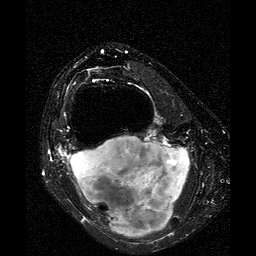
MRI of an extremity soft-tissue mass, one axial slice; slice 17 of 25 in the series (ordered by position); T2-weighted fat-saturated; 256 × 256 image matrix, field of view 160 × 160 mm. Female patient. From the clinical record (not read from this slice): histological type: liposarcoma; site of the primary tumour: right thigh.
Outlined on this slice (outlined manually by an expert reader):
- gross tumour volume (mass): bounding box [x1, y1, x2, y2] px = [69, 136, 189, 239]